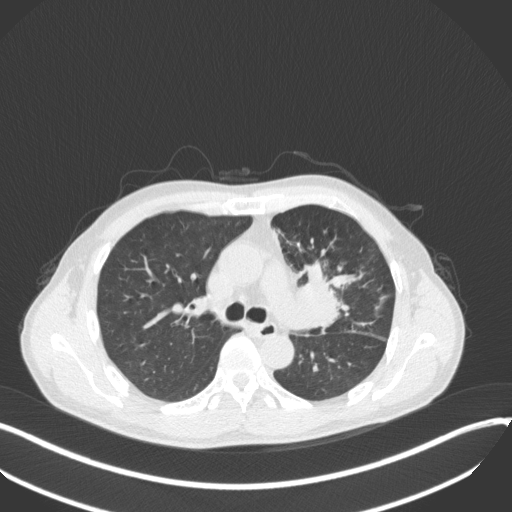
Chest CT, one axial slice; slice 218 of 411 in the series (ordered by position); lung window (W 1500 / L -600 HU); 1 mm slice thickness; 512 × 512 image matrix. Patient: male, 56 years. From the clinical record (not read from this slice): clinical TNM (as recorded): T2a N0 M0.
Structures marked on this image (bounding box drawn by a radiologist):
- lung tumour (recorded histology: squamous cell carcinoma): bounding box [x1, y1, x2, y2] px = [295, 256, 356, 340]